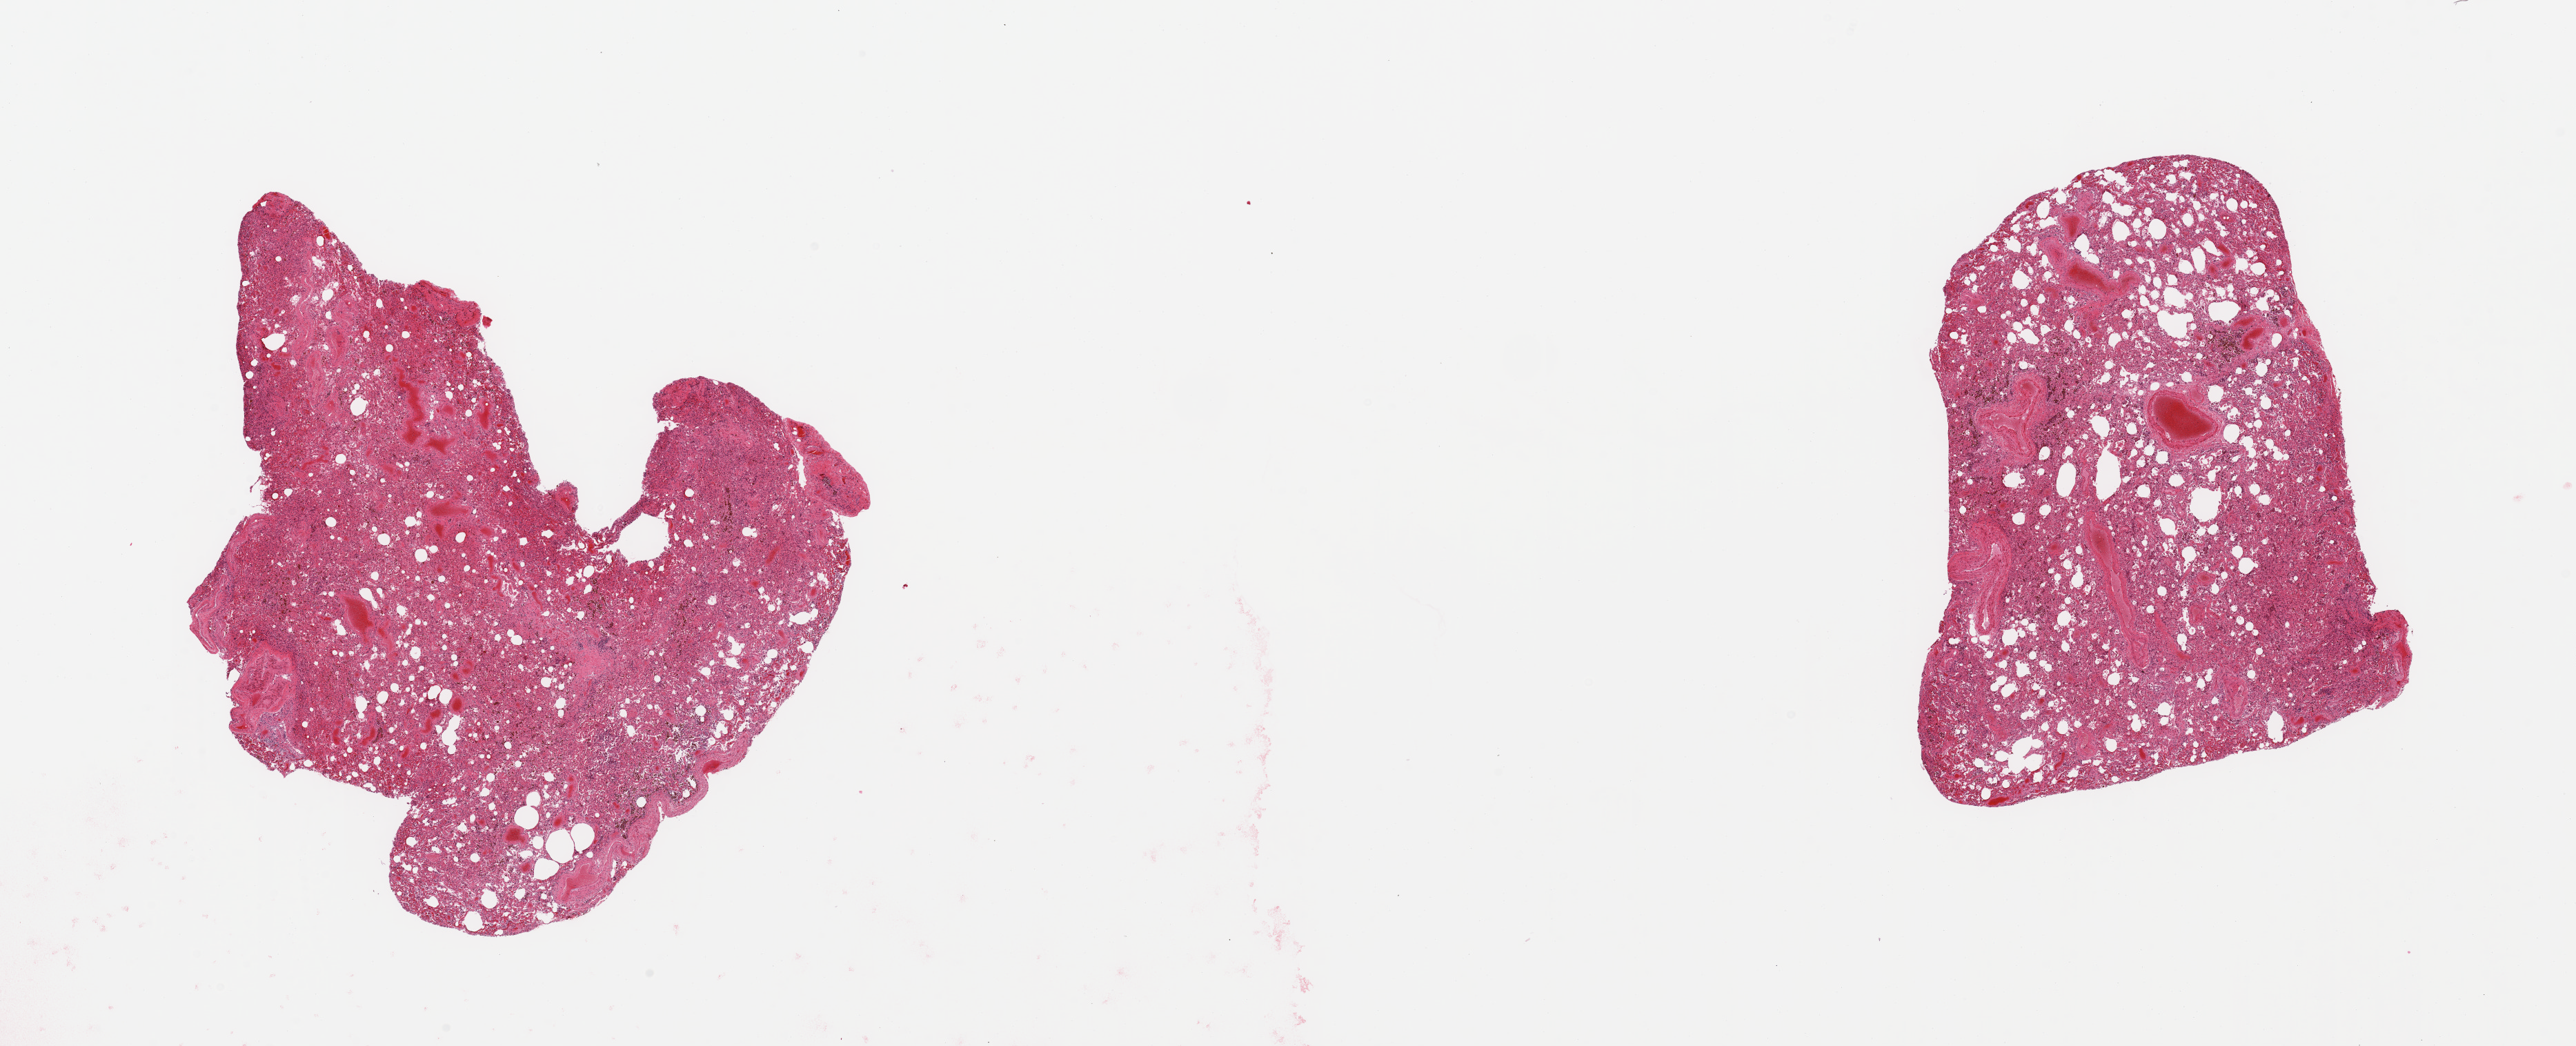
Haematoxylin and eosin whole-slide image, brightfield — shown as a low-resolution overview of the whole scanned area (about 29.5 x 12.0 mm), PAXgene-fixed paraffin-embedded (PFPE) section, target tissue: lung, tissue donor sample. Male donor.
Pathologist's review note for this sample: 2 pieces; moderately congested; numerous alveolar macrophages.